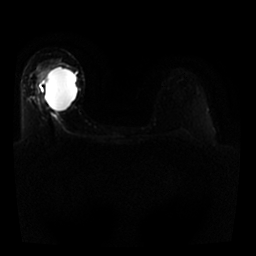
Breast MRI, one axial slice. Diffusion-weighted series; image 2 of 4 stored at this slice position (different b-values; order by instance number). 1.5 T. 4 mm slice thickness. 256 × 256 image matrix. Female patient.
Structures marked on this image (outlined manually by an expert reader):
- tumour on diffusion-weighted imaging: box from (x=43, y=66) to (x=58, y=80) px